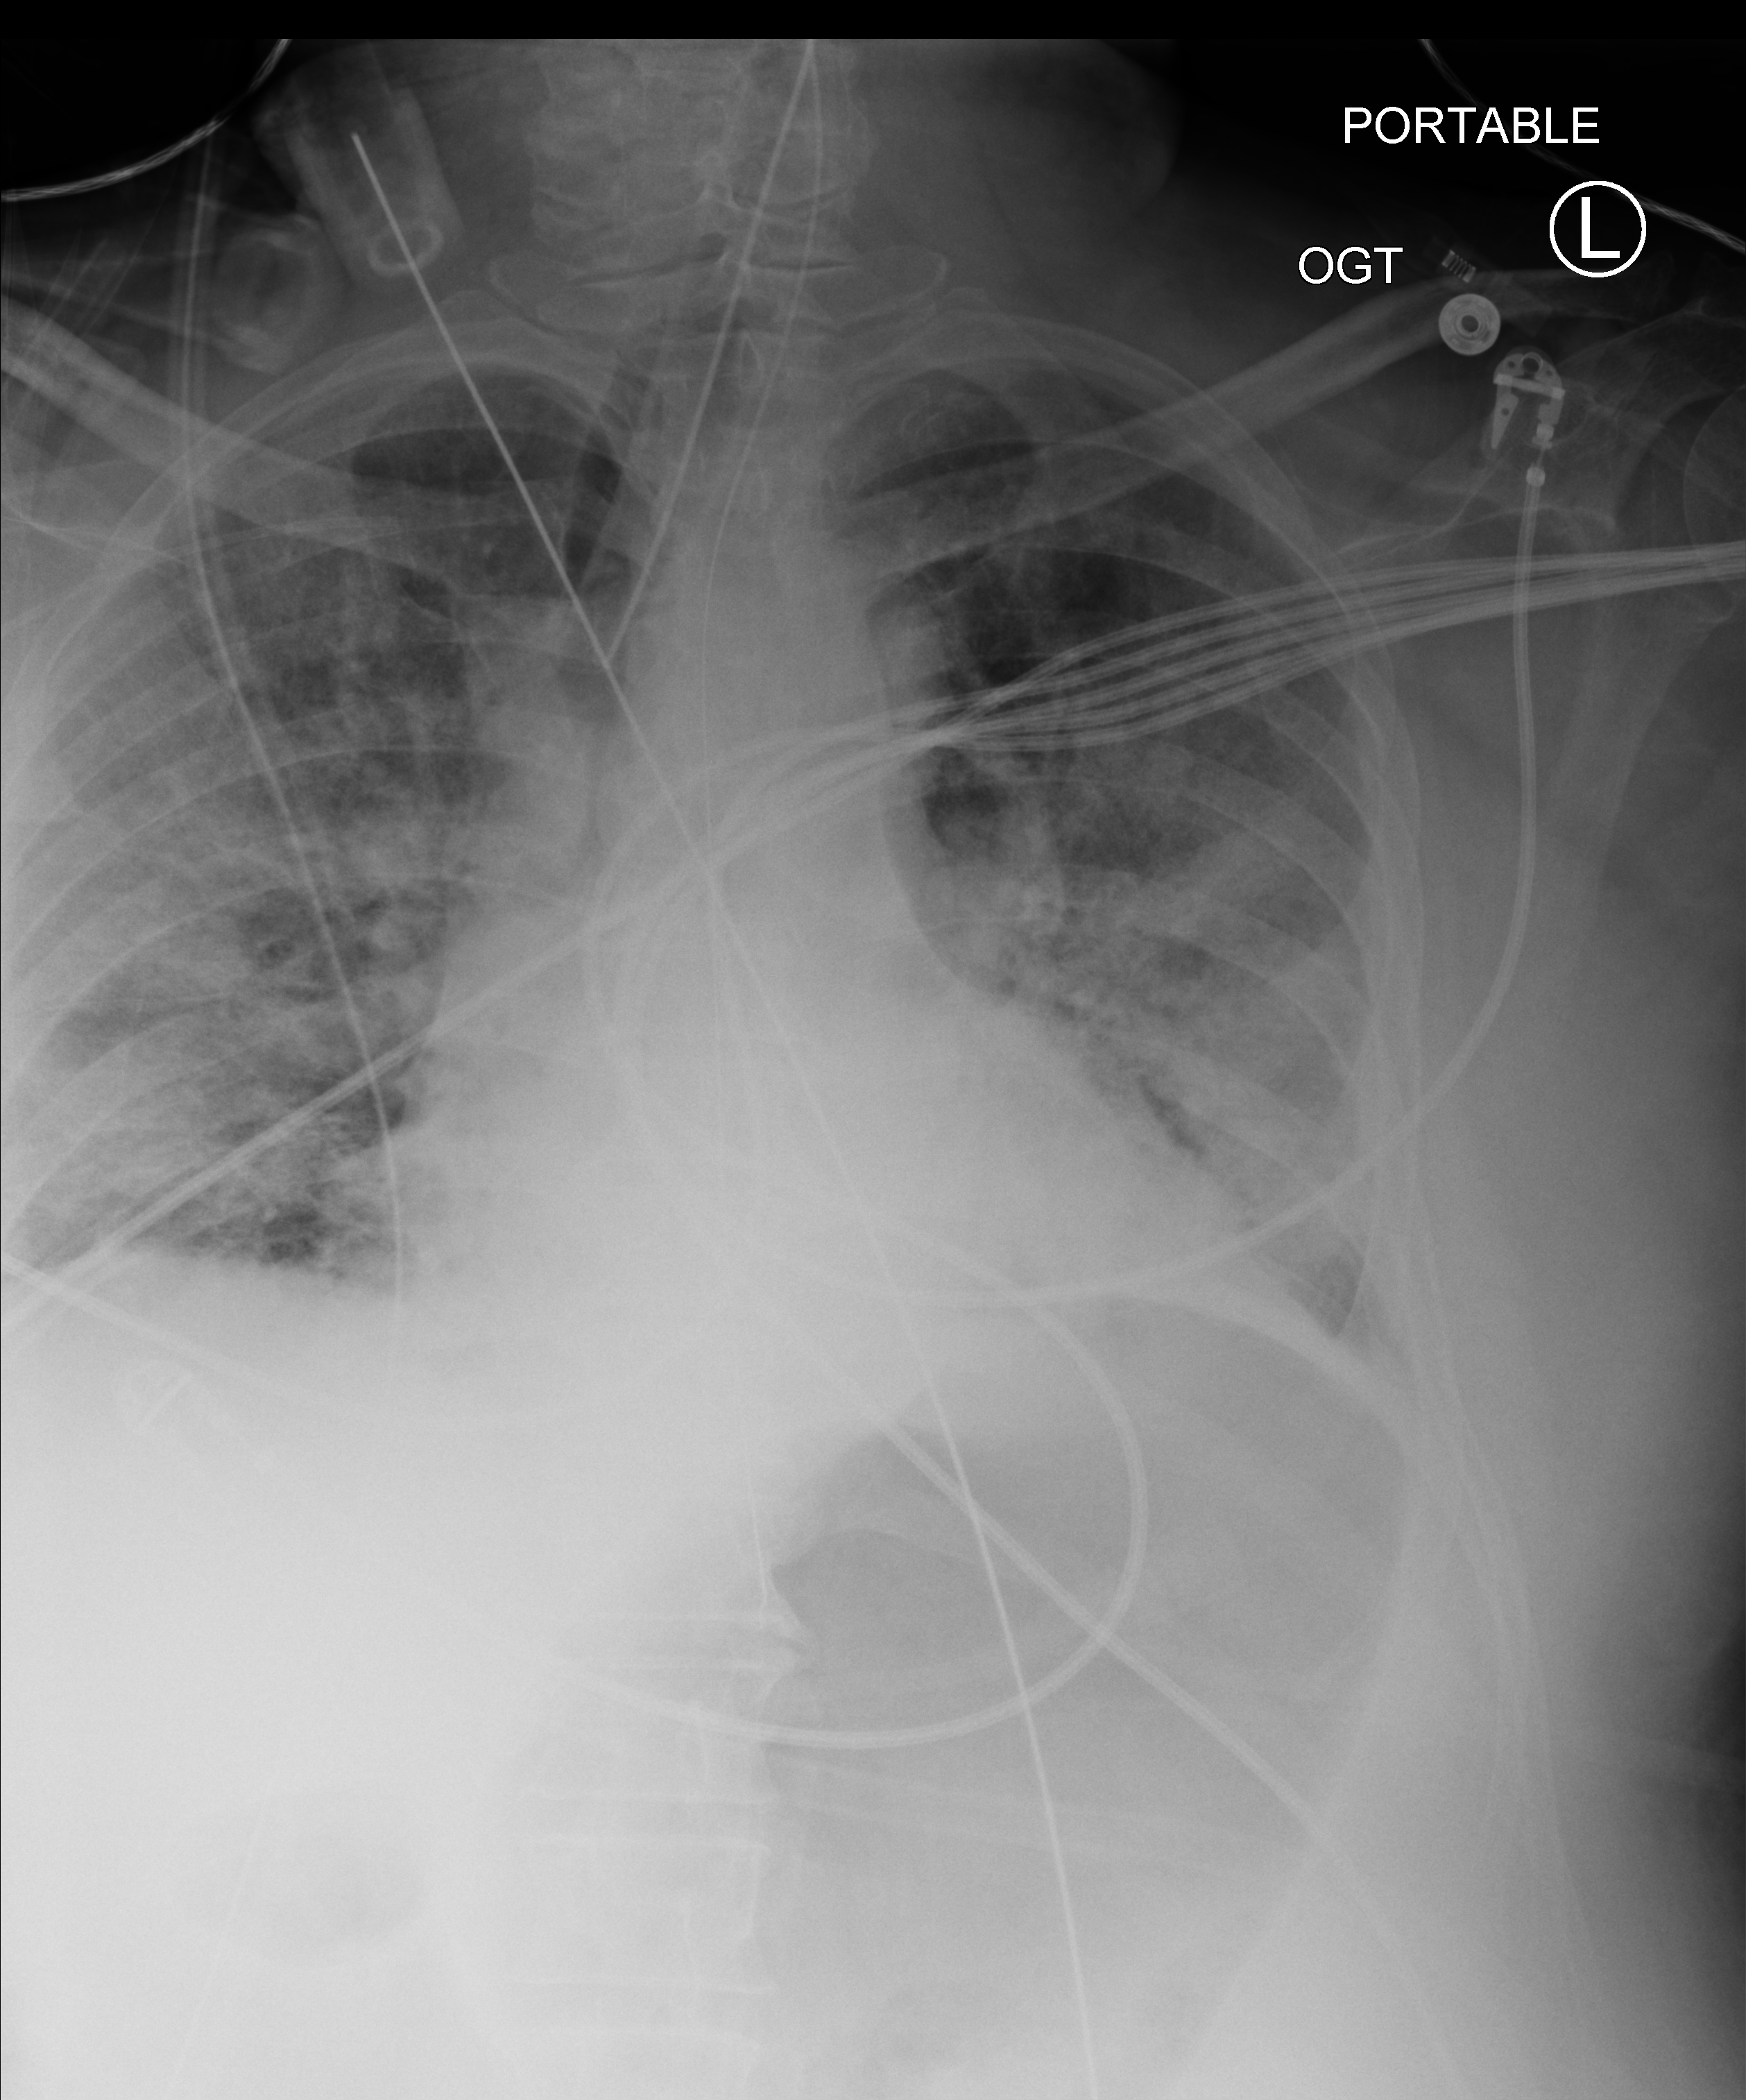
Chest X-ray (portable). Male patient hospitalised with COVID-19, age 60–74 years.
Admission-level facts for this patient (not findings on this image; timing relative to this image not recorded):
- smoking status (admission record): former
- admitted to intensive care during this hospital stay: yes